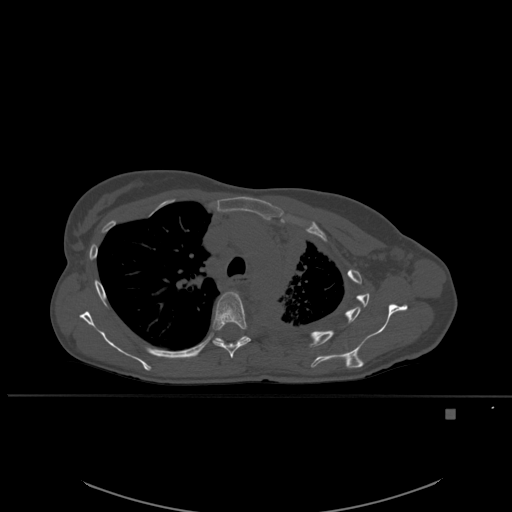
CT including the spine, one axial slice. Slice 397 of 537 in the series (ordered by position). Bone window (W 1800 / L 400 HU). 1.5 mm slice thickness. 512 × 512 image matrix, field of view 440 × 440 mm. Female patient, age 45 years. From the clinical record (not read from this slice): primary cancer: lung.
Outlined on this slice (semi-automatically segmented with operator editing):
- T5 vertebra: bounding box (x1, y1, x2, y2) in pixels: (212, 291, 251, 358)
- T6 vertebra: (213, 336, 247, 344)